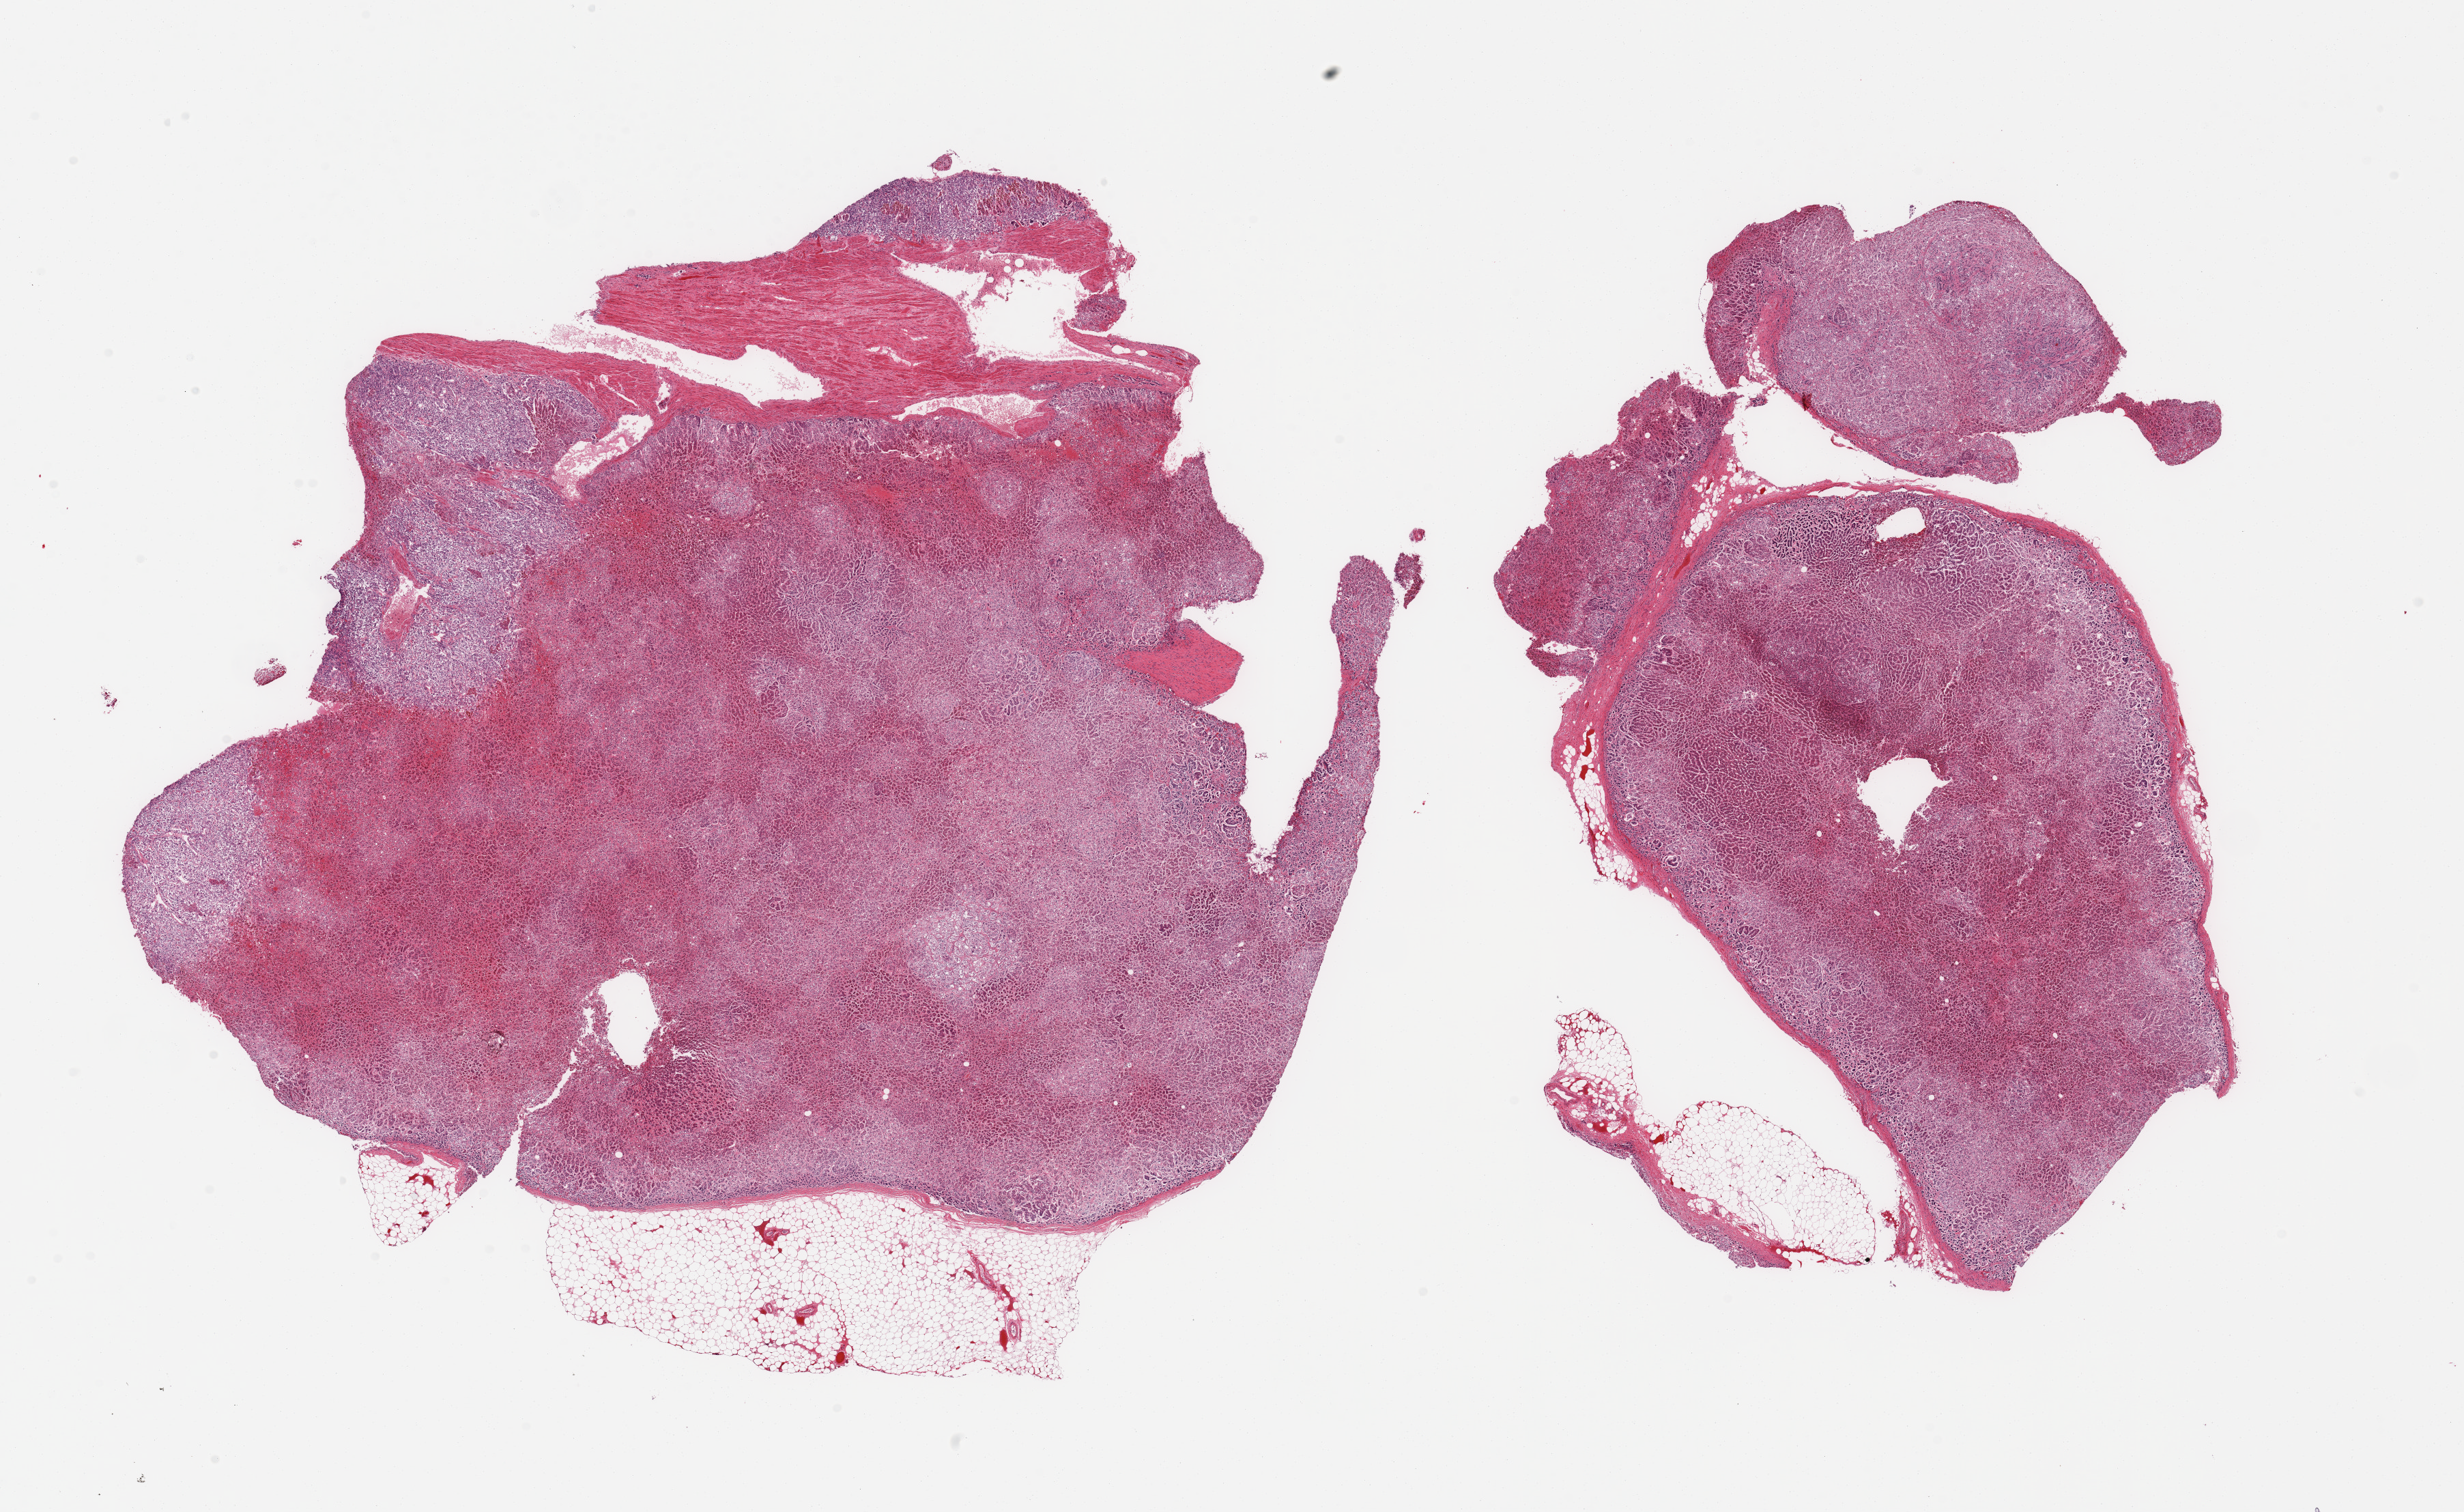
H&E whole-slide image — shown as a low-resolution overview of the whole scanned area (about 28.5 x 17.5 mm, from a 20x scan); PAXgene-fixed paraffin-embedded (PFPE) section; section of adrenal gland (target tissue); tissue donor sample. Donor: male.
Reviewer comment on this tissue sample: 2 pieces; small portion of residual attached fat (5-10%), cortex and medulla.